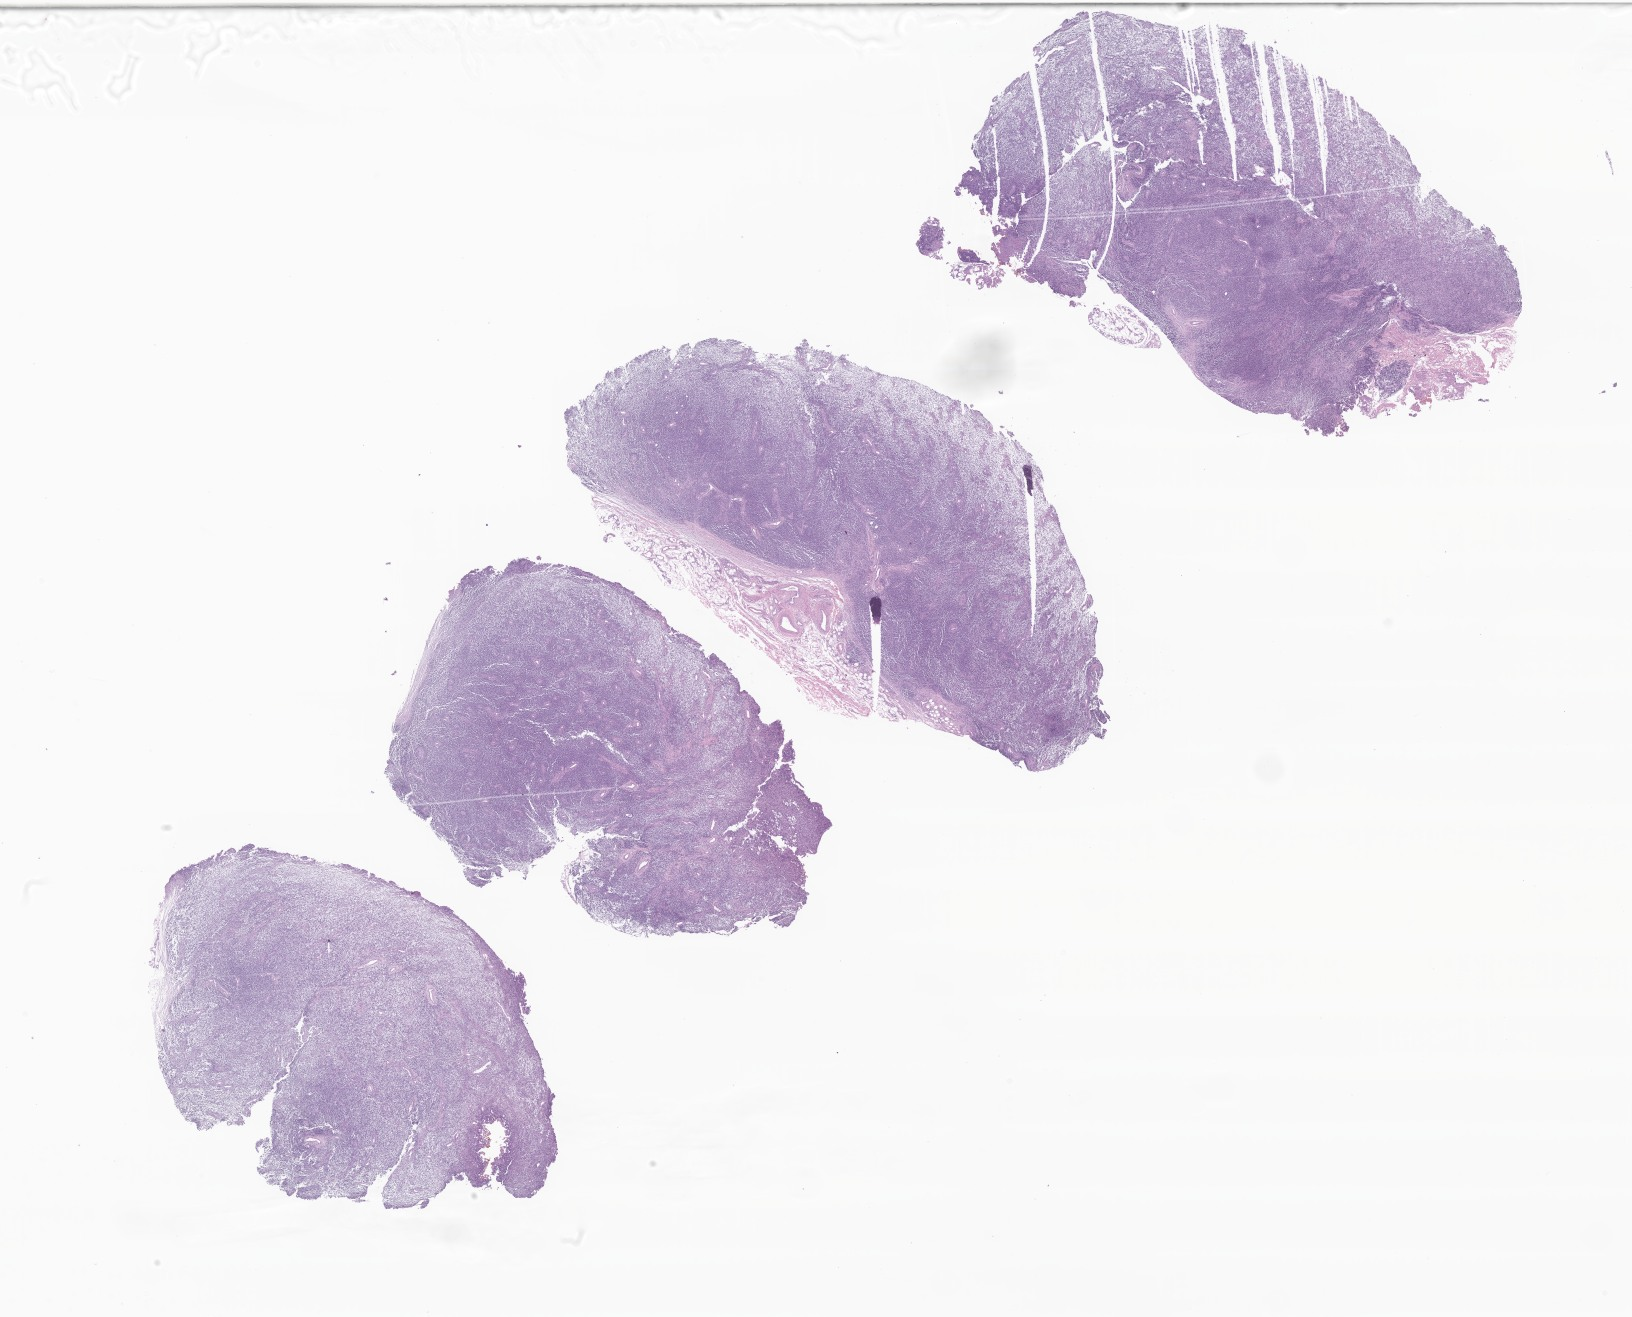
Haematoxylin and eosin whole-slide image of tumor tissue from the orbit, shown as a low-resolution overview of the whole scanned area (about 27.5 x 22.2 mm); formalin-fixed, paraffin-embedded (FFPE) tissue. Male patient, age 64 months (5 years 4 months).
Diagnosis (ICD-O-3 morphology term): Embryonal rhabdomyosarcoma, NOS.